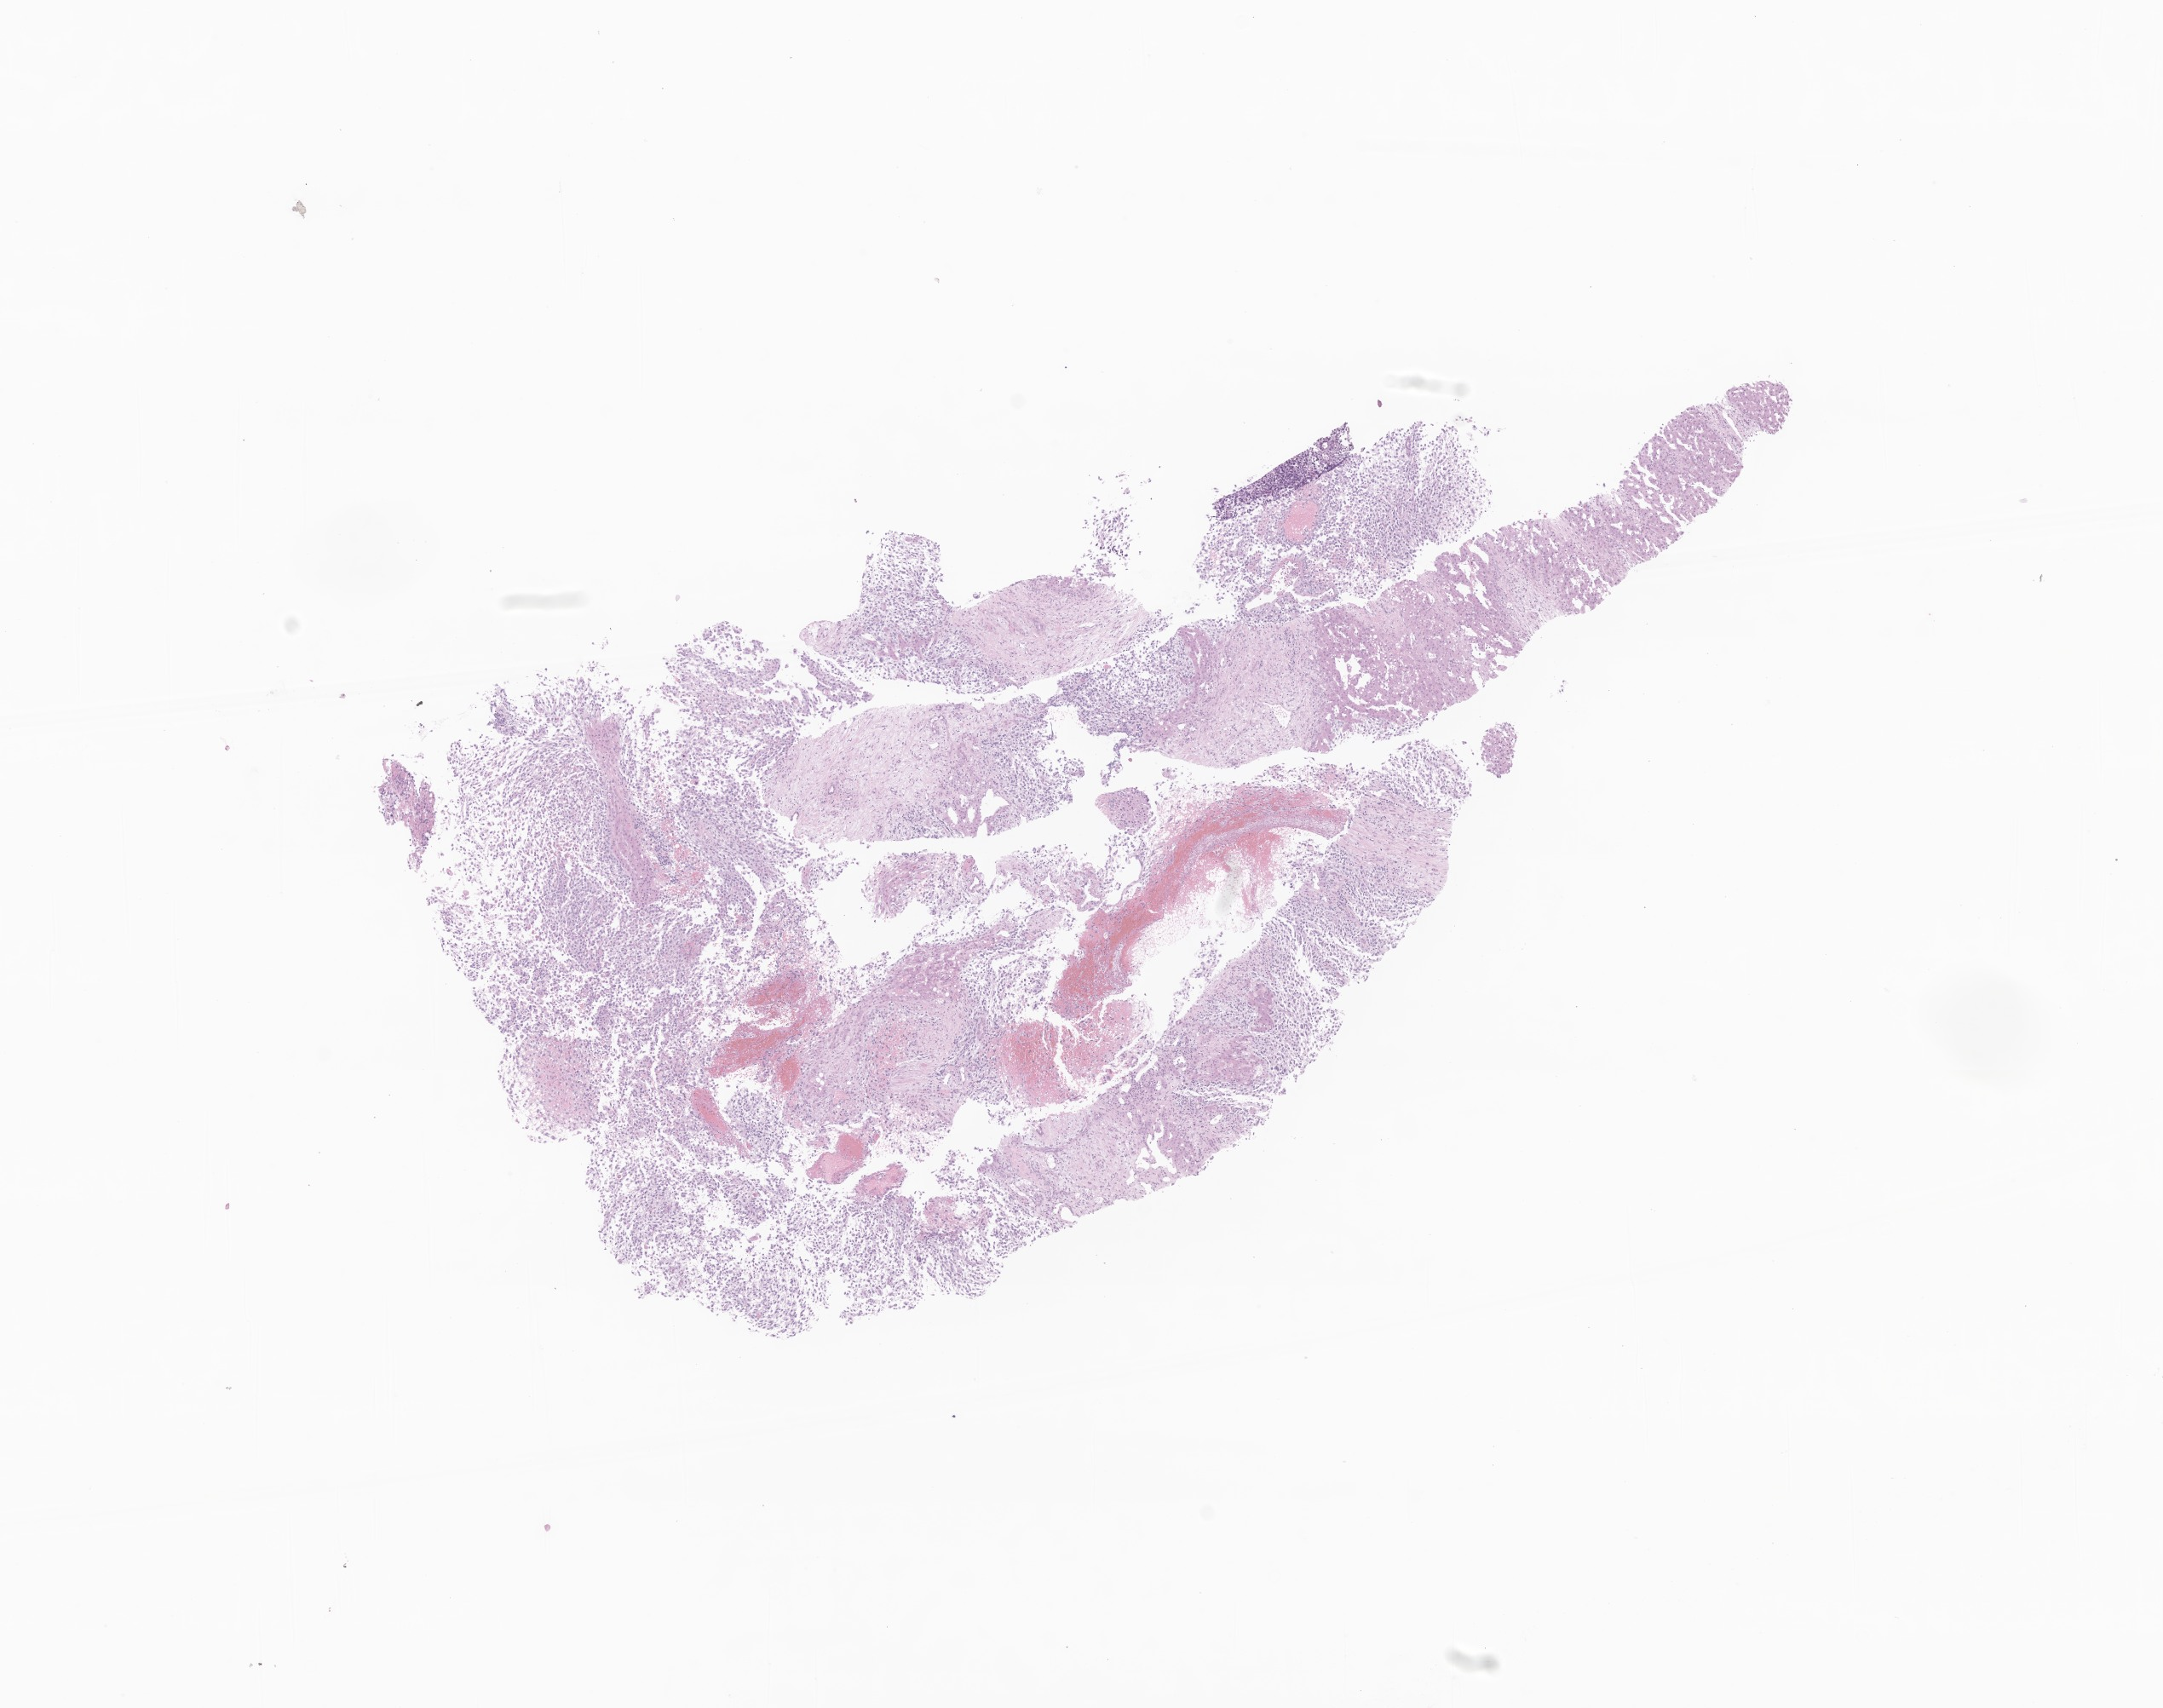
Whole-slide image, haematoxylin and eosin stain of tumor tissue from the liver — low-resolution overview of the scanned area, about 10.7 x 8.5 mm; formalin-fixed paraffin-embedded section. Patient: female, age 111 months (9 years 3 months).
Diagnosis: Embryonal sarcoma.